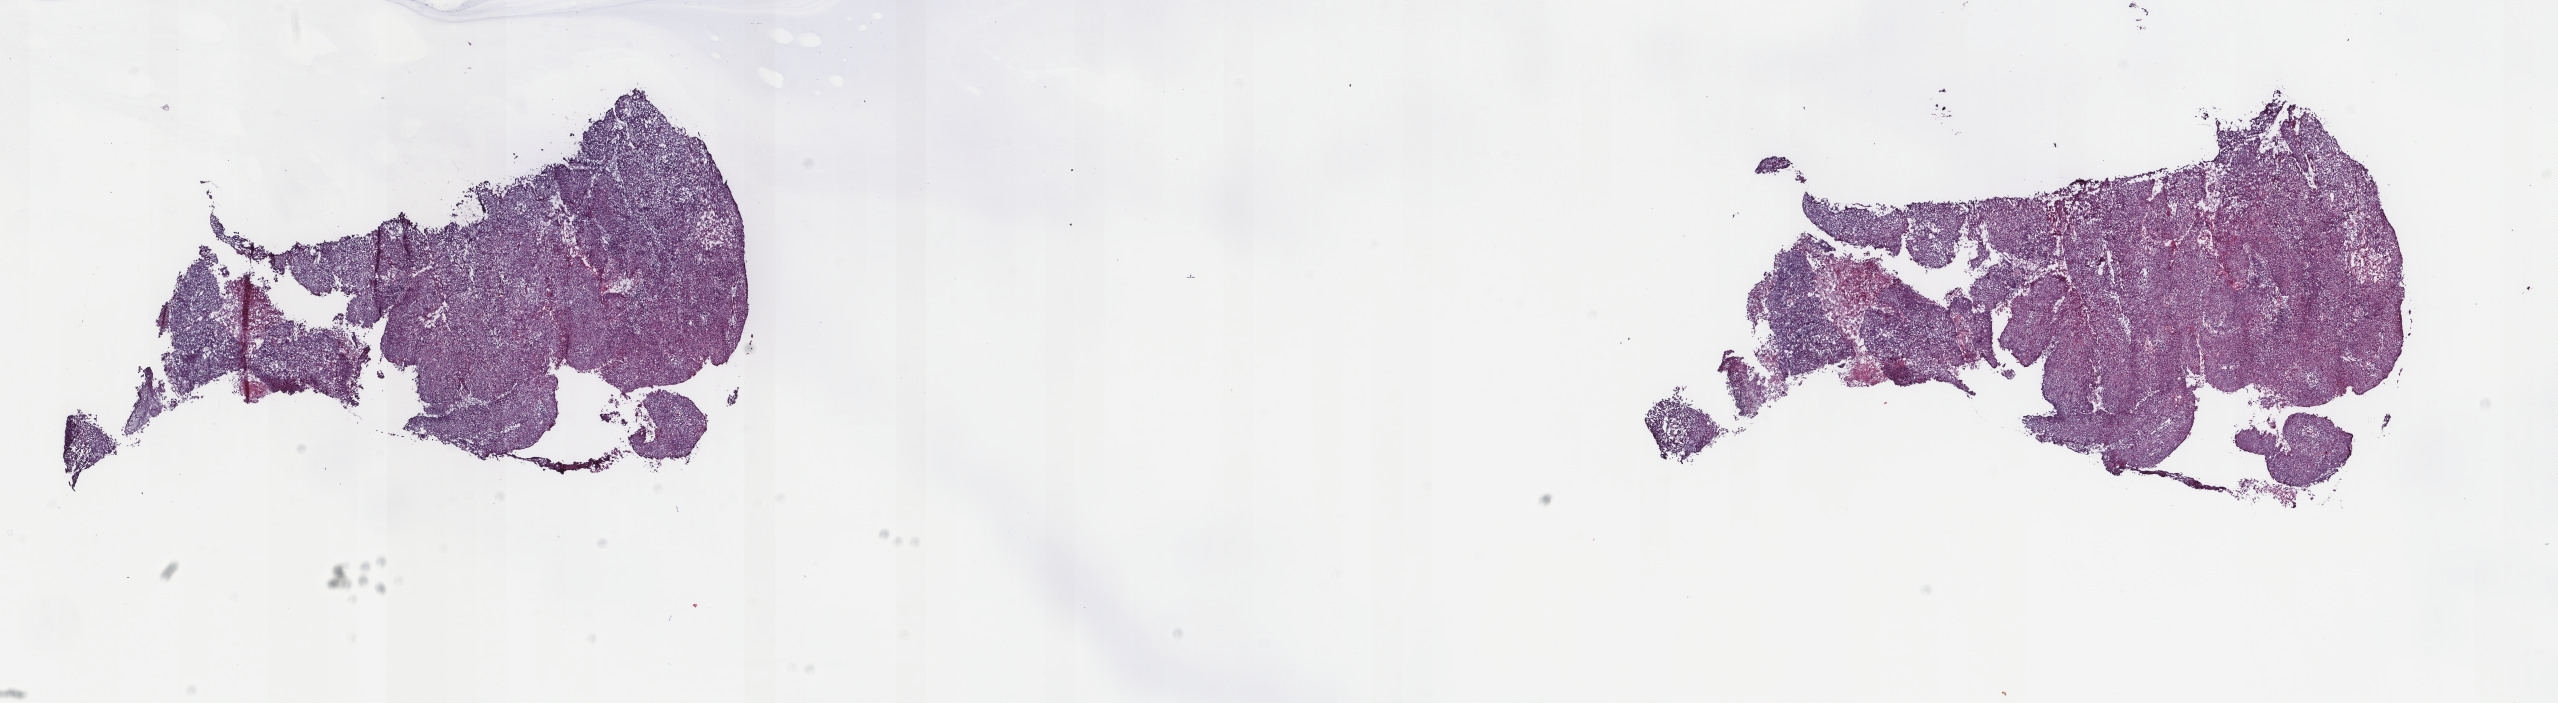
Whole-slide histology image, H&E, shown as a low-resolution overview of the whole scanned area (about 20.3 x 5.6 mm); frozen section from the top of the tissue portion; primary tumour sample from the cervix. Female patient; age at initial diagnosis 65 years. Histologic grade: G2 (moderately differentiated). Composition of this section per pathologist review: tumour cells 70%, tumour nuclei 90%, normal cells 0%, stromal cells 10%, necrosis 20%. Infiltration values recorded for this section: lymphocyte infiltration 10%, monocyte infiltration 0%, neutrophil infiltration 10%.
FIGO stage: IIIB. Diagnosis: Squamous cell carcinoma, keratinizing, NOS (cervix uteri).